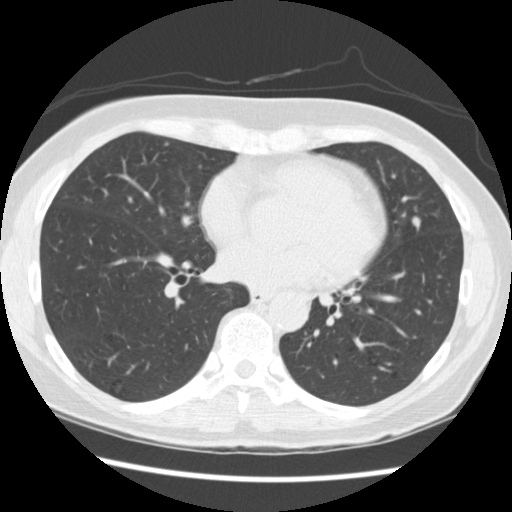
Low-dose screening chest CT, axial slice. Third annual screen. Lung window (W 1500 / L -600 HU). 2.5 mm slice thickness. Slice 142 of 262 in the series. Female, age 60 years at enrolment. Current smoker at enrolment.
Expert reader's lesion annotation, bounding box [x1, y1, x2, y2] px = [393, 205, 436, 245]. Screening reader's record for this exam (one nodule recorded; not confirmed to be the boxed lesion): non-calcified nodule or mass ≥4 mm, lingula, 6 × 5 mm, smooth margins, soft tissue attenuation, pre-existing on the prior screen: yes; interval growth: yes. Participant outcome: lung cancer diagnosed 209 days after this screen — adenocarcinoma, NOS, lingula, poorly differentiated (G3), stage IA (AJCC 6th edition), 6 mm at pathology.